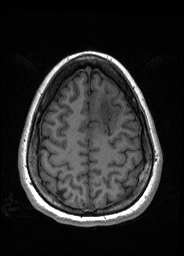
Pre-operative brain MRI before brain-tumour surgery, one axial slice; slice 51 of 176 in the series (ordered by position); T1-weighted post-contrast; 1 mm slice thickness; 184 × 256 image matrix, field of view 180 × 250 mm. Case-level facts recorded for this patient, not image findings: histopathology: Oligodendroglioma; WHO grade: 2; IDH mutation: yes; tumour location: Left Frontal.
Outlined on this slice (expert manual segmentation):
- tumour: bounding box [x1, y1, x2, y2] px = [91, 96, 117, 135]